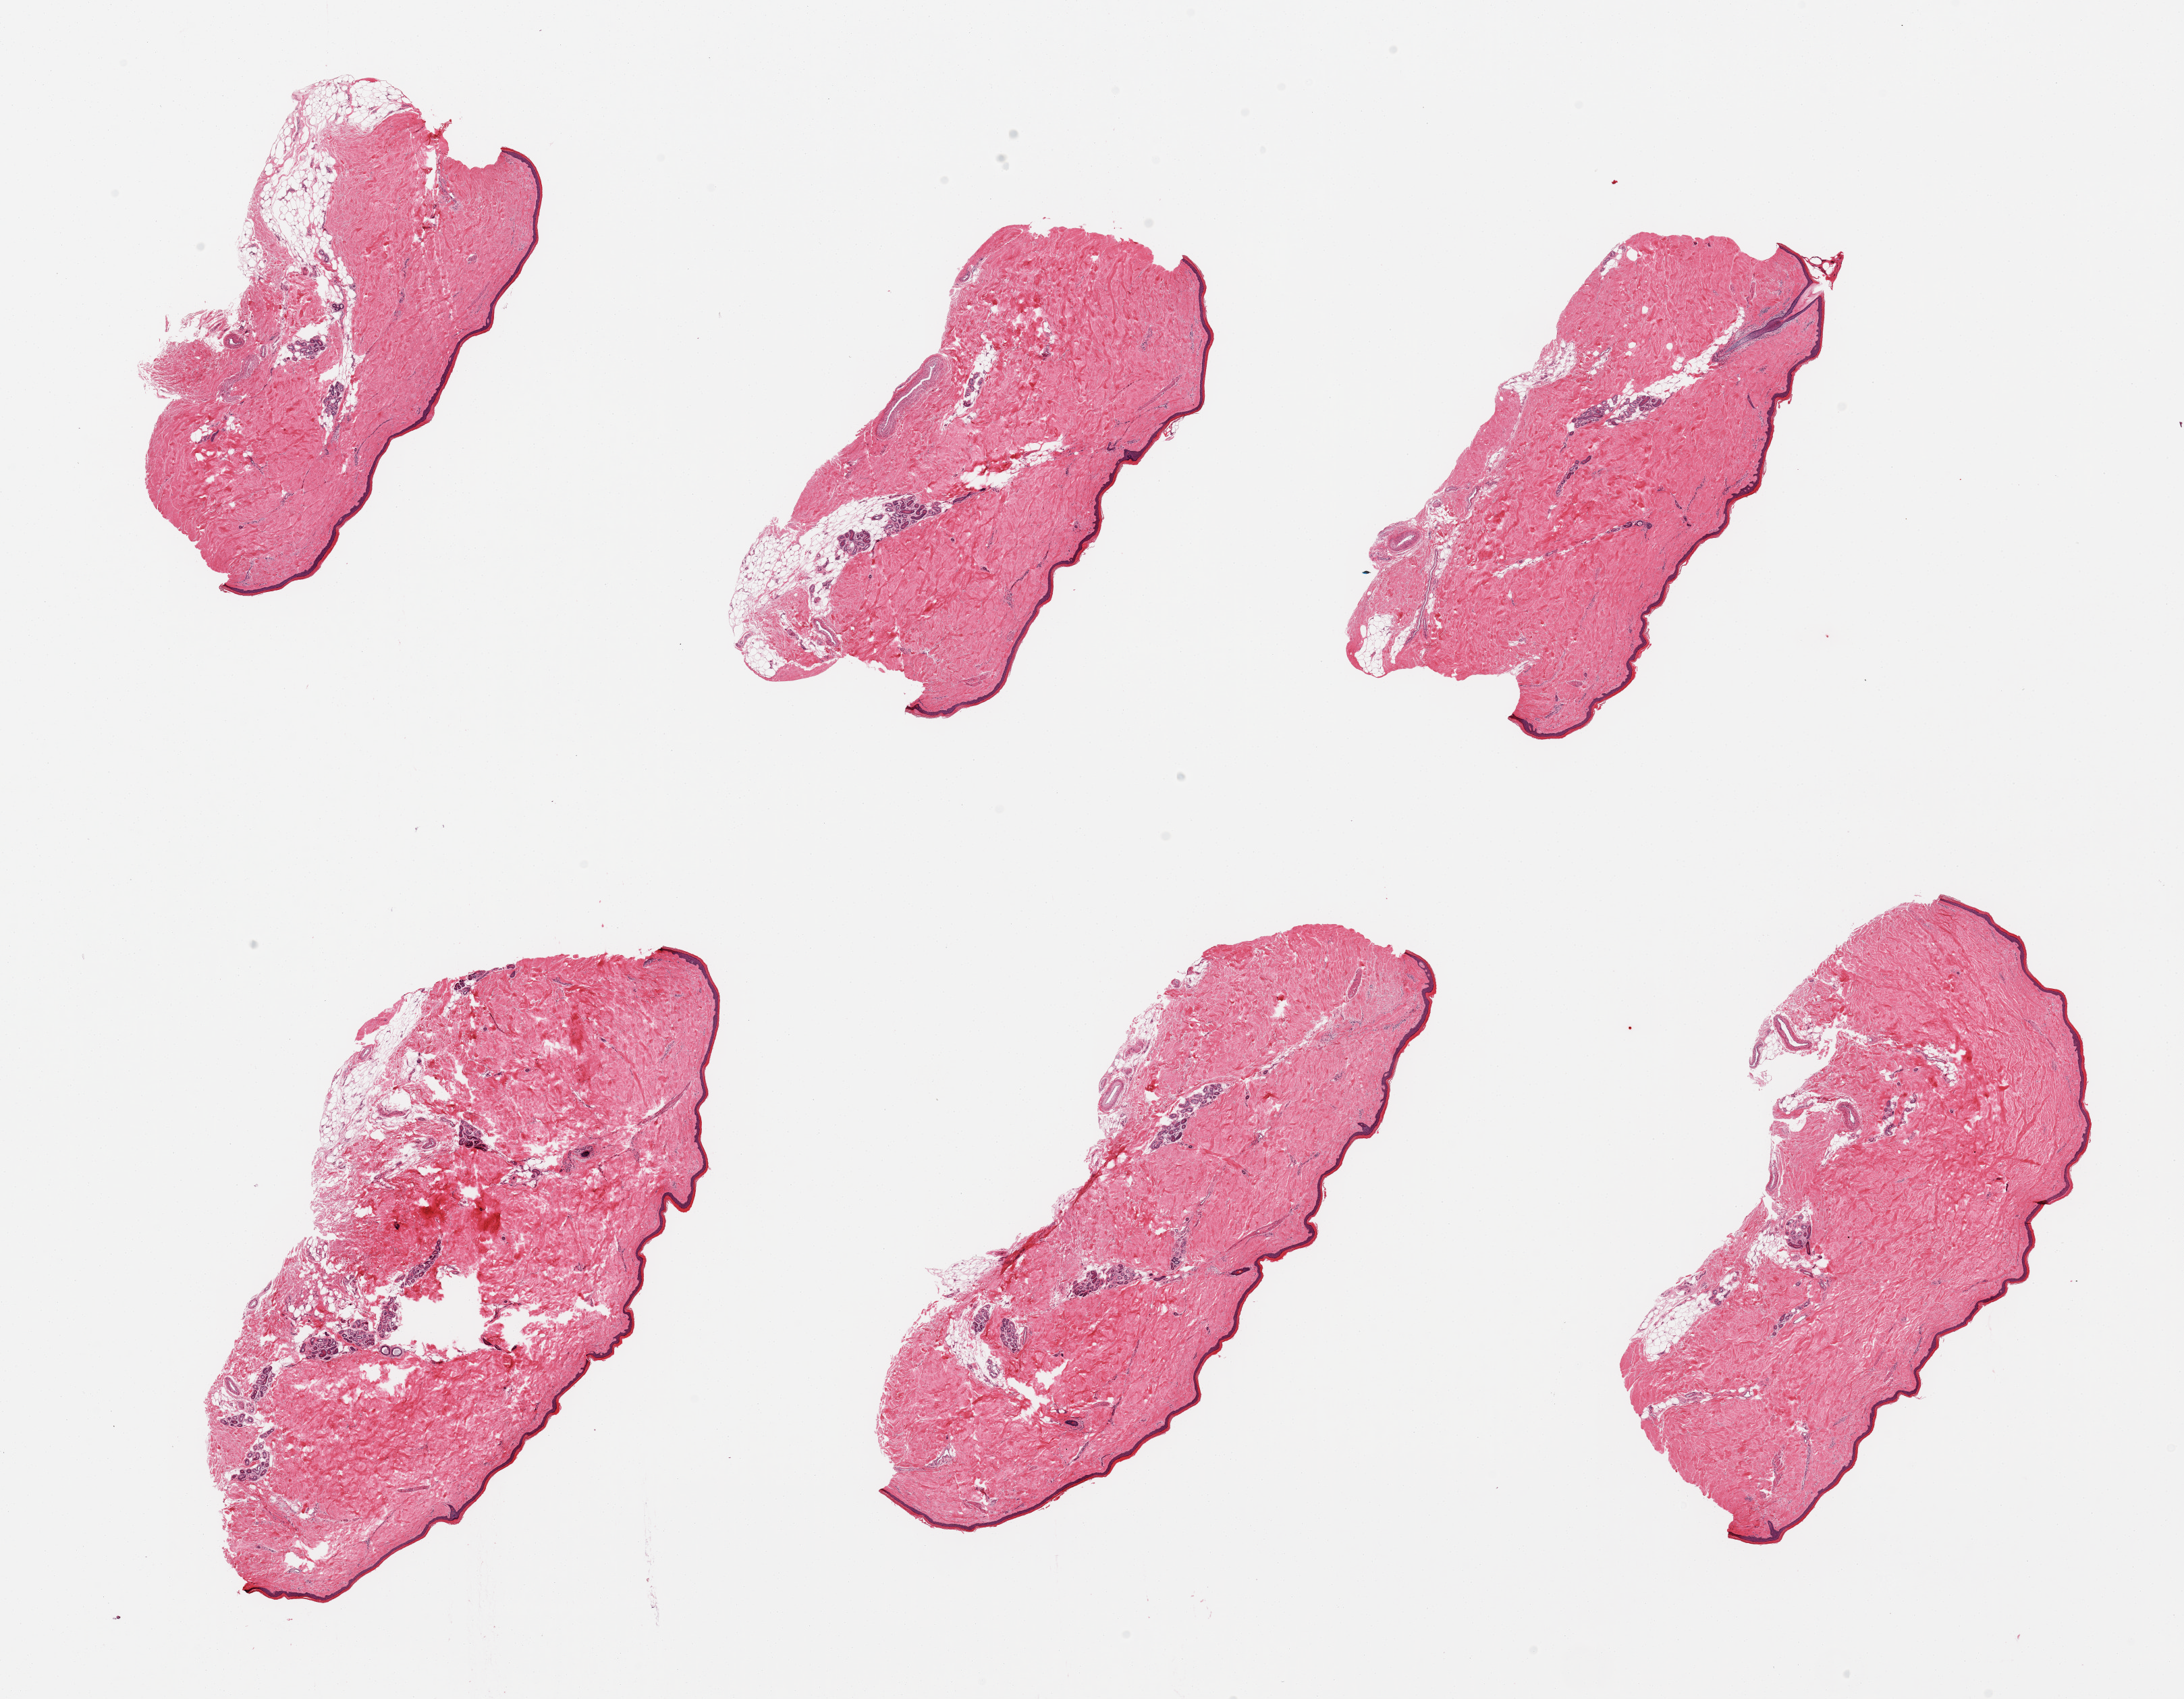
Whole-slide image, hematoxylin and eosin (H&E) stain, brightfield, a low-resolution overview of the entire scanned area, about 25.6 x 19.9 mm (acquisition: 20x scan); PAXgene-fixed, paraffin-embedded tissue; target tissue: skin of lower leg; tissue donor sample. Donor: male.
- reviewer comment on this tissue sample: 6 pieces; includes 5-10% fat, epidermis measures 36 microns in thickness